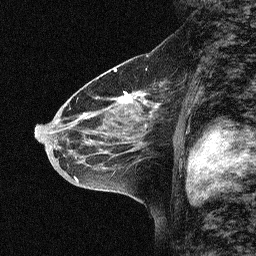
Breast MRI (dynamic contrast-enhanced), one sagittal slice; position 37 of 64 along the scan axis; dynamic contrast-enhanced study with each time point stored as its own series, time point 2 of 3 at this slice position (early post-contrast, ordered by acquisition time); 1.5 T; TE 4.5 ms, TR 11 ms; 2.06 mm slice thickness; 256 × 256 image matrix, field of view 200 × 200 mm. Female patient, age 46 years. Case-level facts recorded for this patient, not image findings: setting: breast cancer imaged before/during neoadjuvant chemotherapy; receptor status: HER2-positive.
Structures marked on this image (semi-automatically segmented with operator editing):
- analysis volume of interest (the breast-tissue region the enhancement analysis was run in; not a lesion): bounding box [x1, y1, x2, y2] px = [46, 51, 180, 169]
- tumour enhancement mask (voxels above the 90 % enhancement threshold inside the analysis volume of interest): [120, 95, 145, 105]